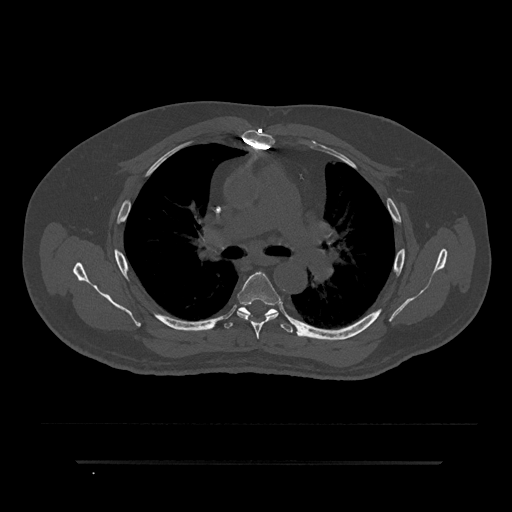
CT including the spine, one axial slice; position 559 of 797 along the scan axis; reconstruction kernel Br40s/3; 120 kVp; bone window (W 1800 / L 400 HU); 0.5 mm slice thickness; 512 × 512 image matrix, field of view 464 × 464 mm. Patient: male, 59 years. From the clinical record (not read from this slice): primary cancer: bile ducts.
Structures marked on this image (semi-automatically segmented with operator editing):
- T5 vertebra: bounding box <237,272,280,339> (left, top, right, bottom; pixels)
- T6 vertebra: <224,299,293,333>